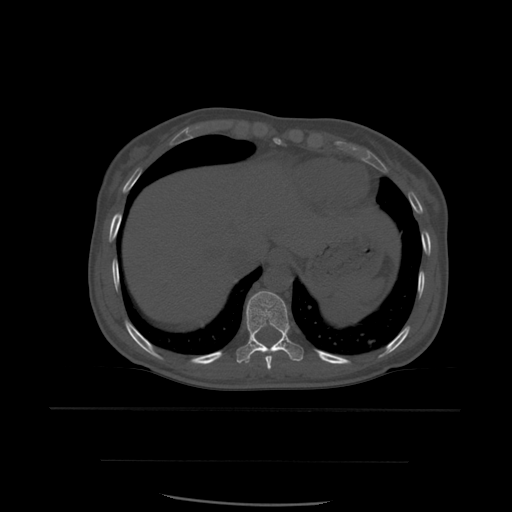
CT including the spine, one axial slice; position 320 of 574 along the scan axis; bone window (W 1800 / L 400 HU); 1.25 mm slice thickness; 512 × 512 image matrix. Patient age 48 years. From the clinical record (not read from this slice): primary cancer: lung.
Annotated regions visible in this slice (semi-automatically segmented with operator editing):
- T10 vertebra: bounding box [x1, y1, x2, y2] px = [236, 291, 304, 364]
- T9 vertebra: [265, 347, 285, 370]